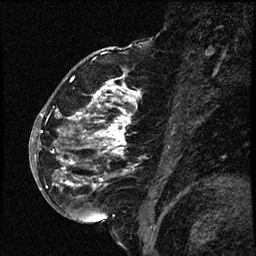
Breast MRI (dynamic contrast-enhanced), one sagittal slice. Position 35 of 66 along the scan axis. Dynamic contrast-enhanced study with each time point stored as its own series, time point 2 of 3 at this slice position (early post-contrast, ordered by acquisition time). 1.5 T. TE 4.2 ms, TR 17.6 ms. 2 mm slice thickness. 256 × 256 image matrix, field of view 200 × 200 mm. Female patient. Case-level facts recorded for this patient, not image findings: setting: breast cancer imaged before/during neoadjuvant chemotherapy; receptor status: HER2-positive.
Outlined on this slice (semi-automatically segmented with operator editing):
- analysis volume of interest (the breast-tissue region the enhancement analysis was run in; not a lesion): bounding box <52,69,149,209> (left, top, right, bottom; pixels)
- tumour enhancement mask (voxels above the 100 % enhancement threshold inside the analysis volume of interest): <56,80,140,186>